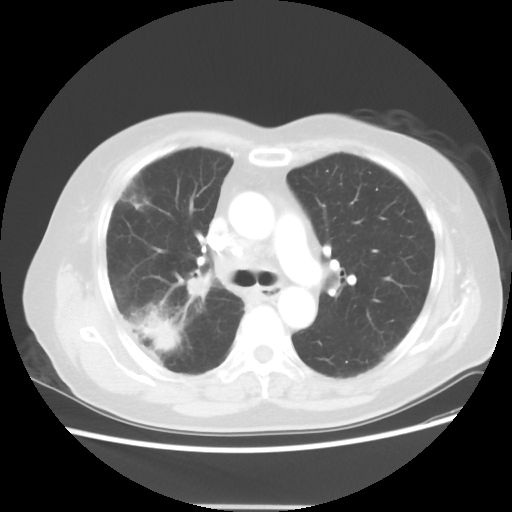
Chest CT, one axial slice; reconstruction kernel STANDARD; 120 kVp; lung window (W 1500 / L -600 HU); 512 × 512 image matrix. Patient: female, 72 years. From the clinical record (not read from this slice): clinical TNM (as recorded): T2 N1 M0; histopathological grade: G1.
Outlined on this slice (rectangle marked by the reading radiologist):
- lung tumour (recorded histology: adenocarcinoma): box from (x=140, y=311) to (x=176, y=351) px